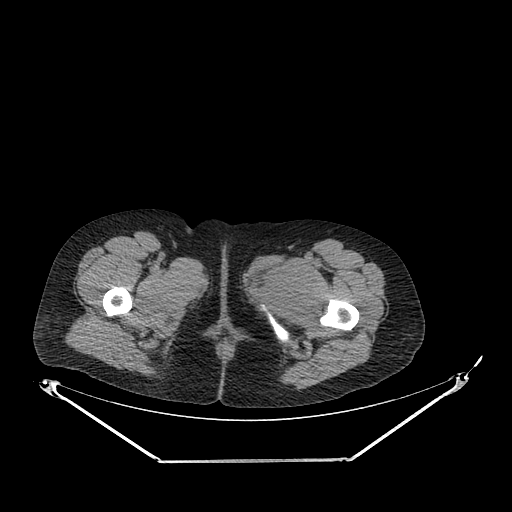
CT of an extremity soft-tissue mass (from a PET/CT study), one axial slice. Slice 254 of 267 in the series (ordered by position). Reconstruction kernel SOFT. Soft-tissue window (W 400 / L 40 HU). 3.75 mm slice thickness. 512 × 512 image matrix. Female patient. From the clinical record (not read from this slice): histological type: pleiomorphic leiomyosarcoma; grade: intermediate; site of the primary tumour: left thigh.
Structures marked on this image (expert contour drawn on MRI and transferred to this co-registered scan by the dataset authors):
- gross tumour volume including surrounding oedema: box from (x=247, y=257) to (x=316, y=311) px
- gross tumour volume (mass): (x=251, y=258)–(x=316, y=311)